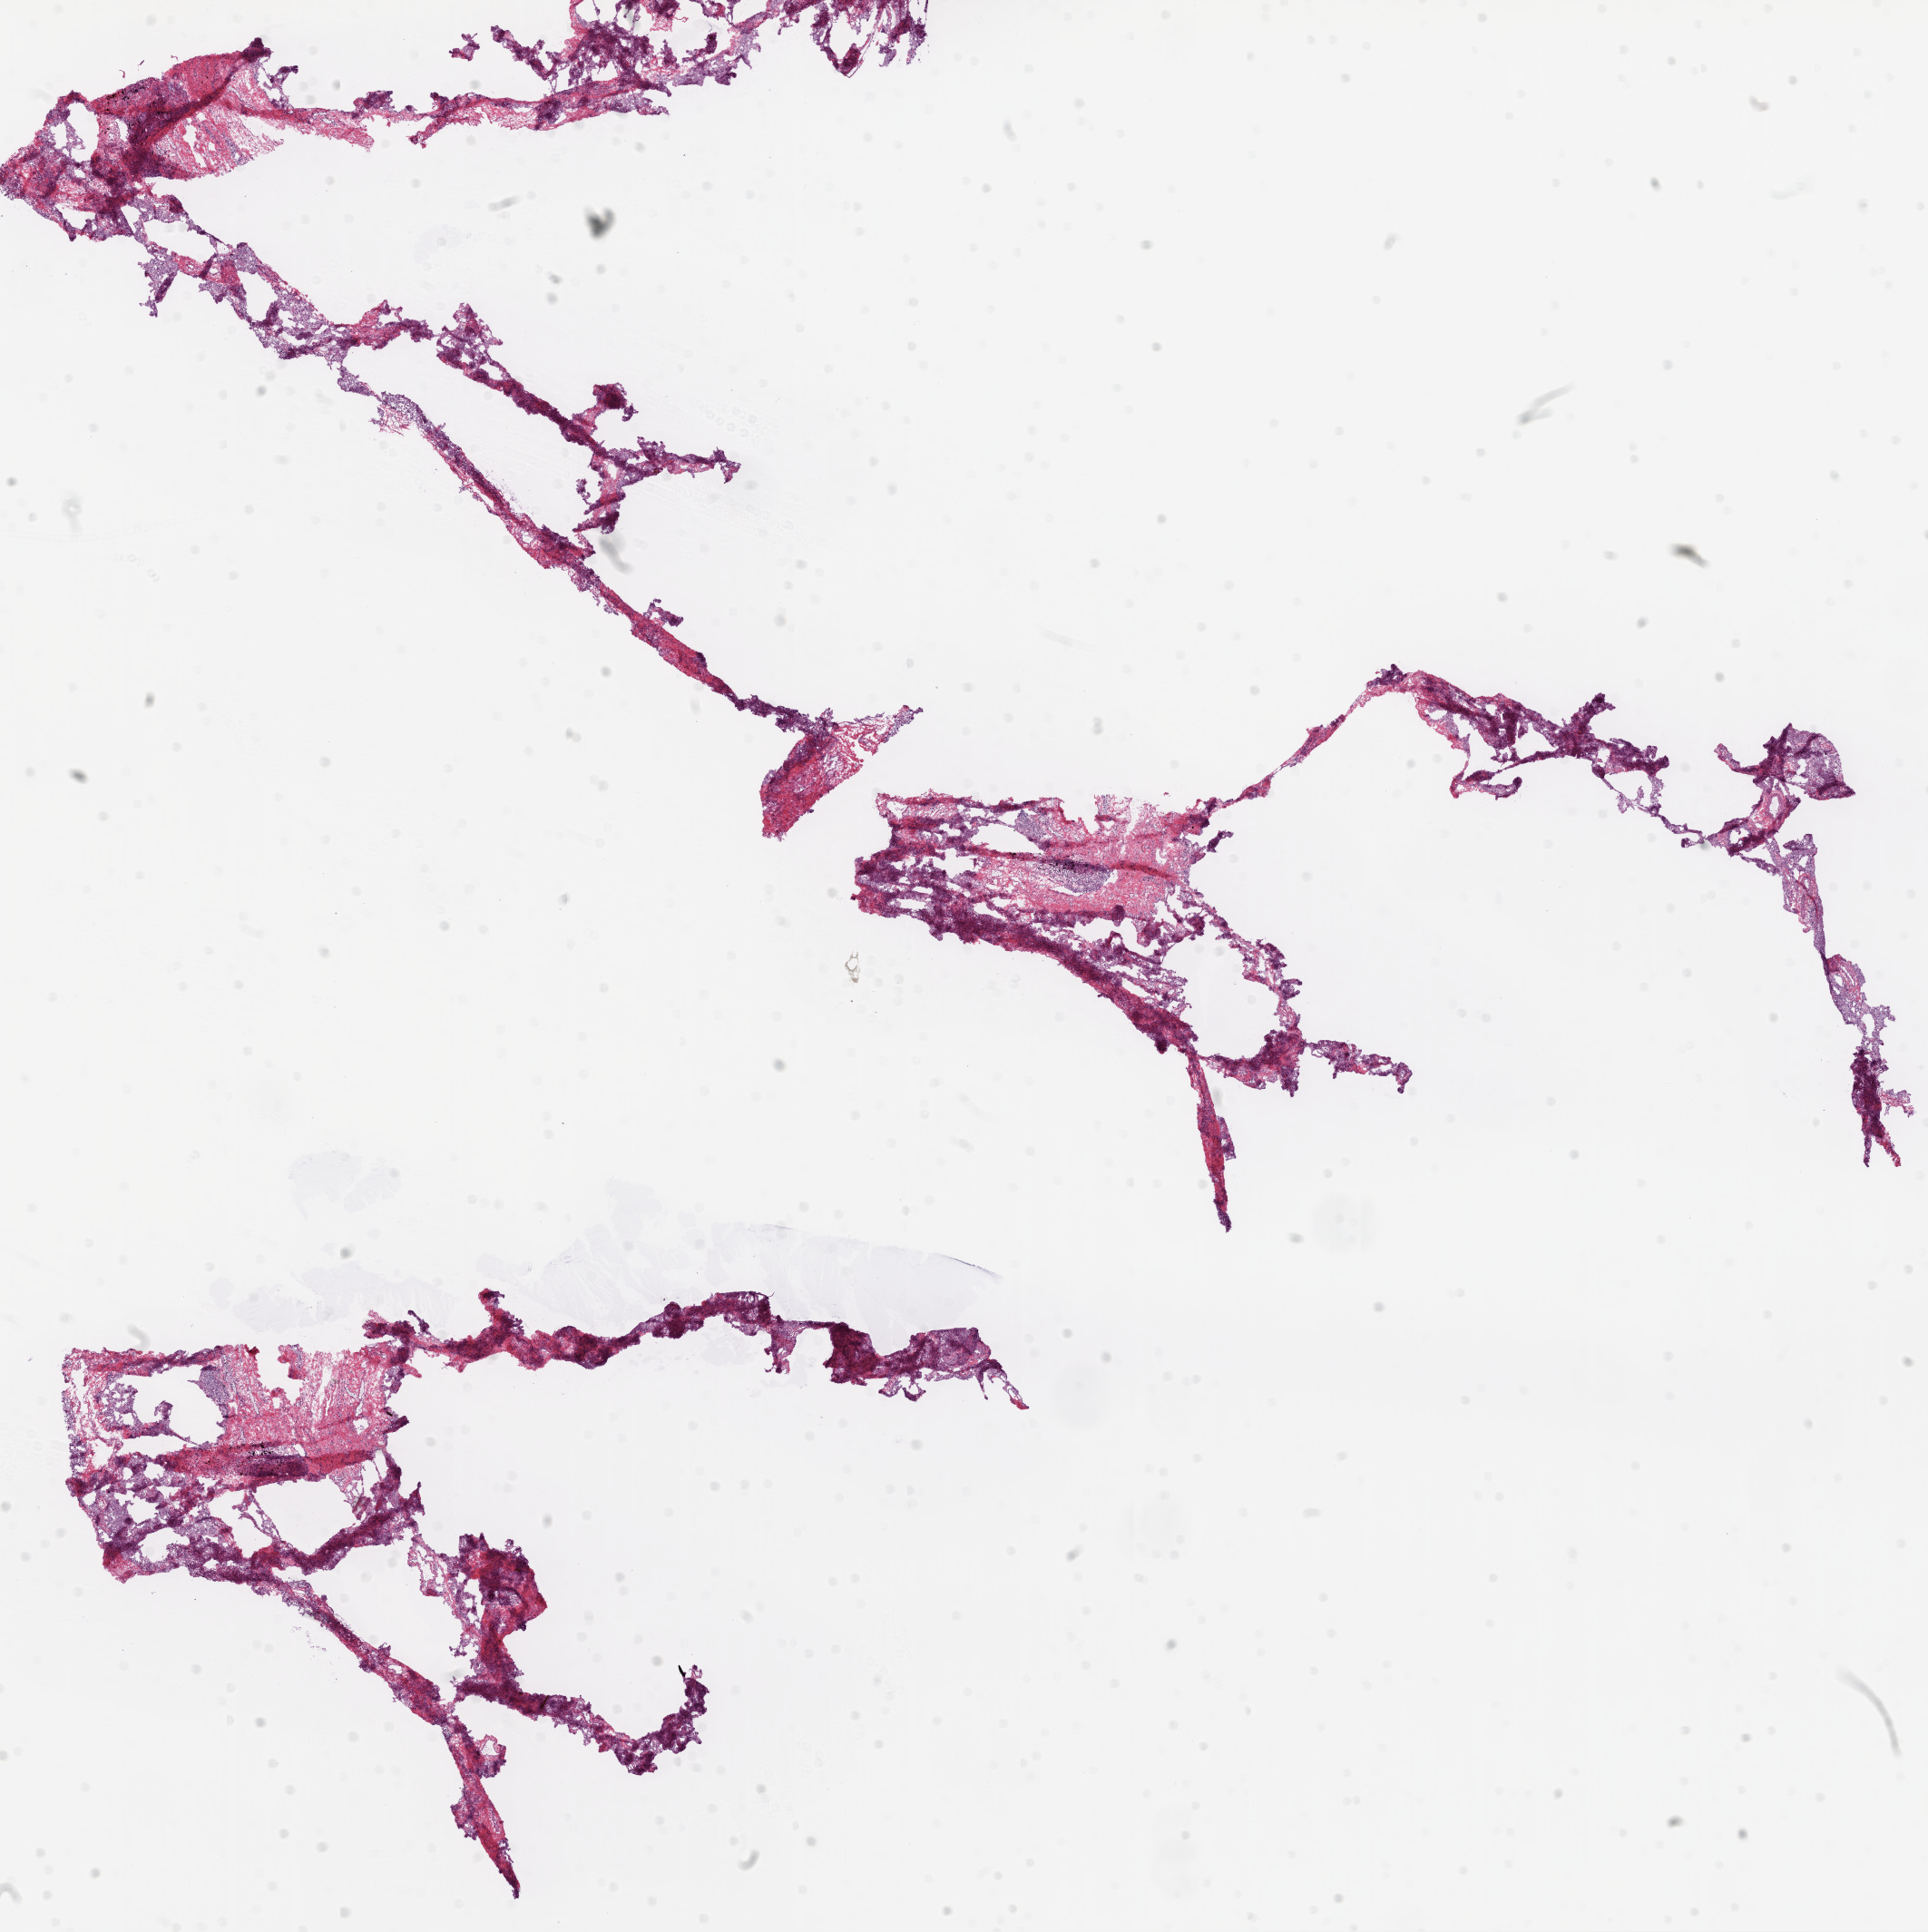
Whole-slide histology image, Hematoxylin and eosin (H&E) stained — shown as a low-resolution overview of the whole scanned area (about 17.1 x 17.1 mm); frozen section from the top of the tissue portion; lung, solid tissue normal (non-tumour tissue) sample. Female, age 63 years at initial diagnosis.
This section: solid tissue normal sample (biorepository sample class). Patient diagnosis: Squamous cell carcinoma, NOS (upper lobe, lung).